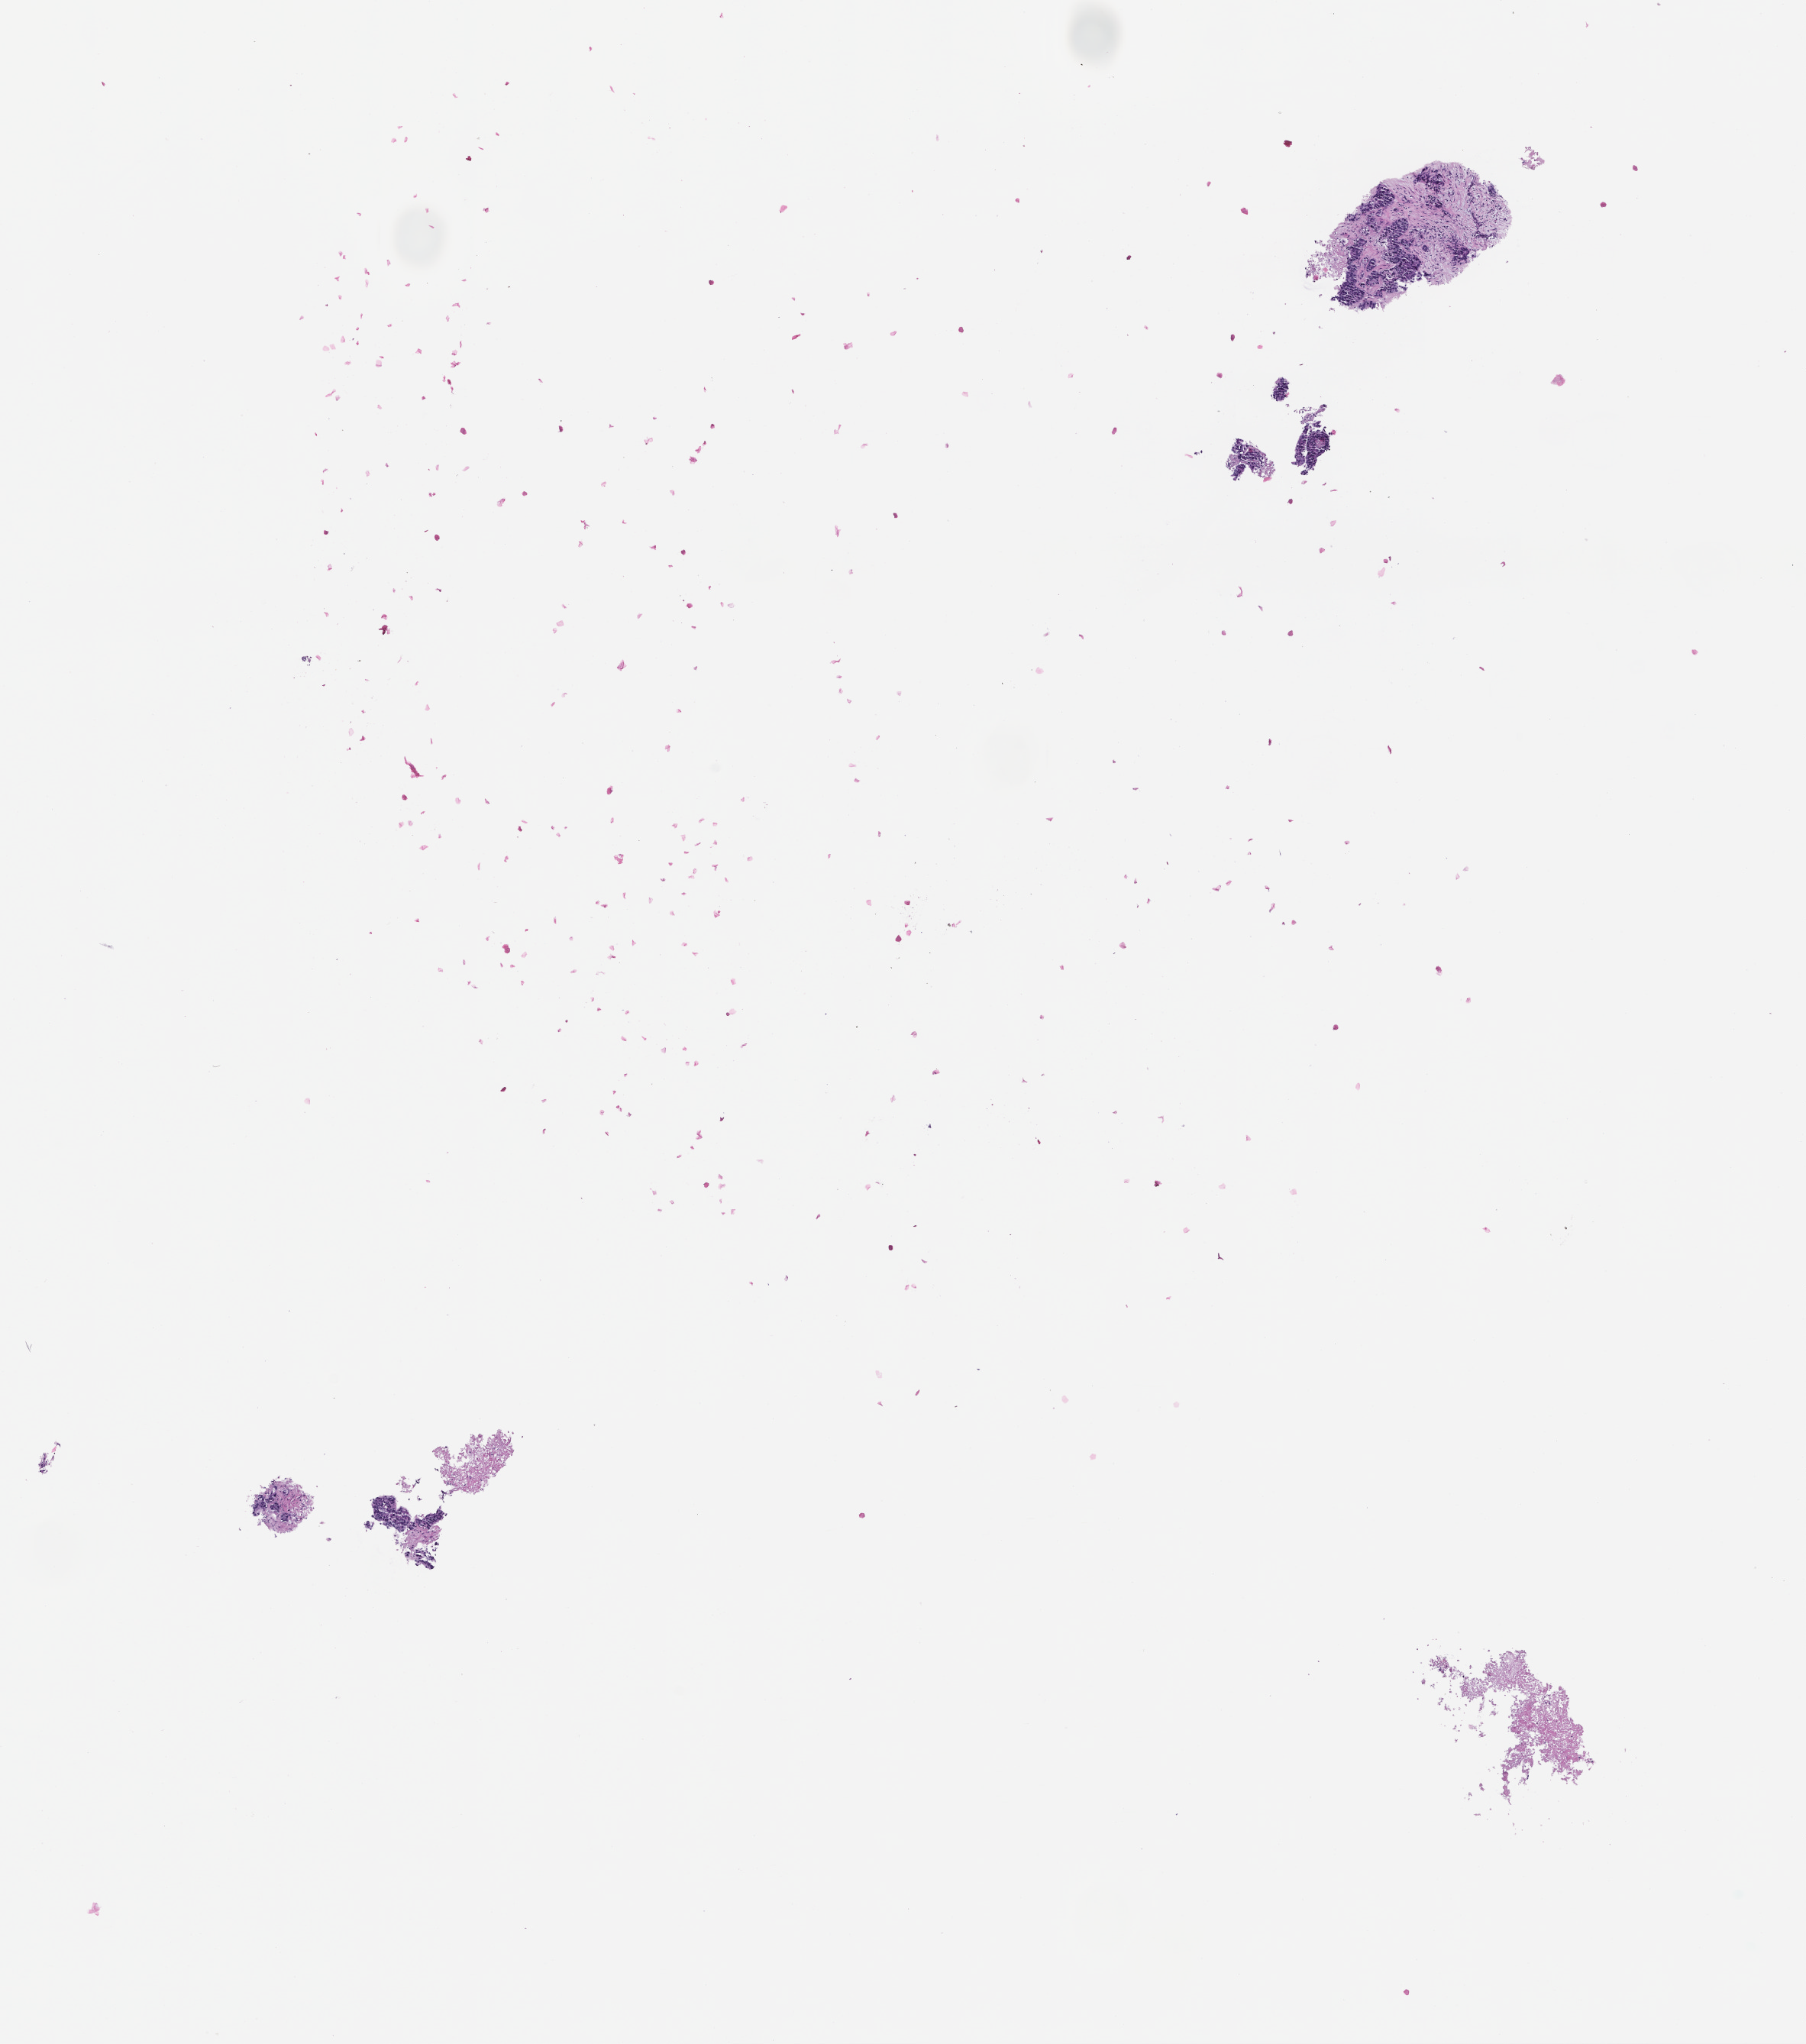
Digitized H&E-stained section — low-resolution overview of the scanned area, about 9.5 x 10.8 mm. Formalin-fixed paraffin-embedded section. Collected at baseline (before treatment). Patient sex: female.
This section: metastatic tumor tissue. Patient diagnosis (primary): Colorectal Carcinoma.